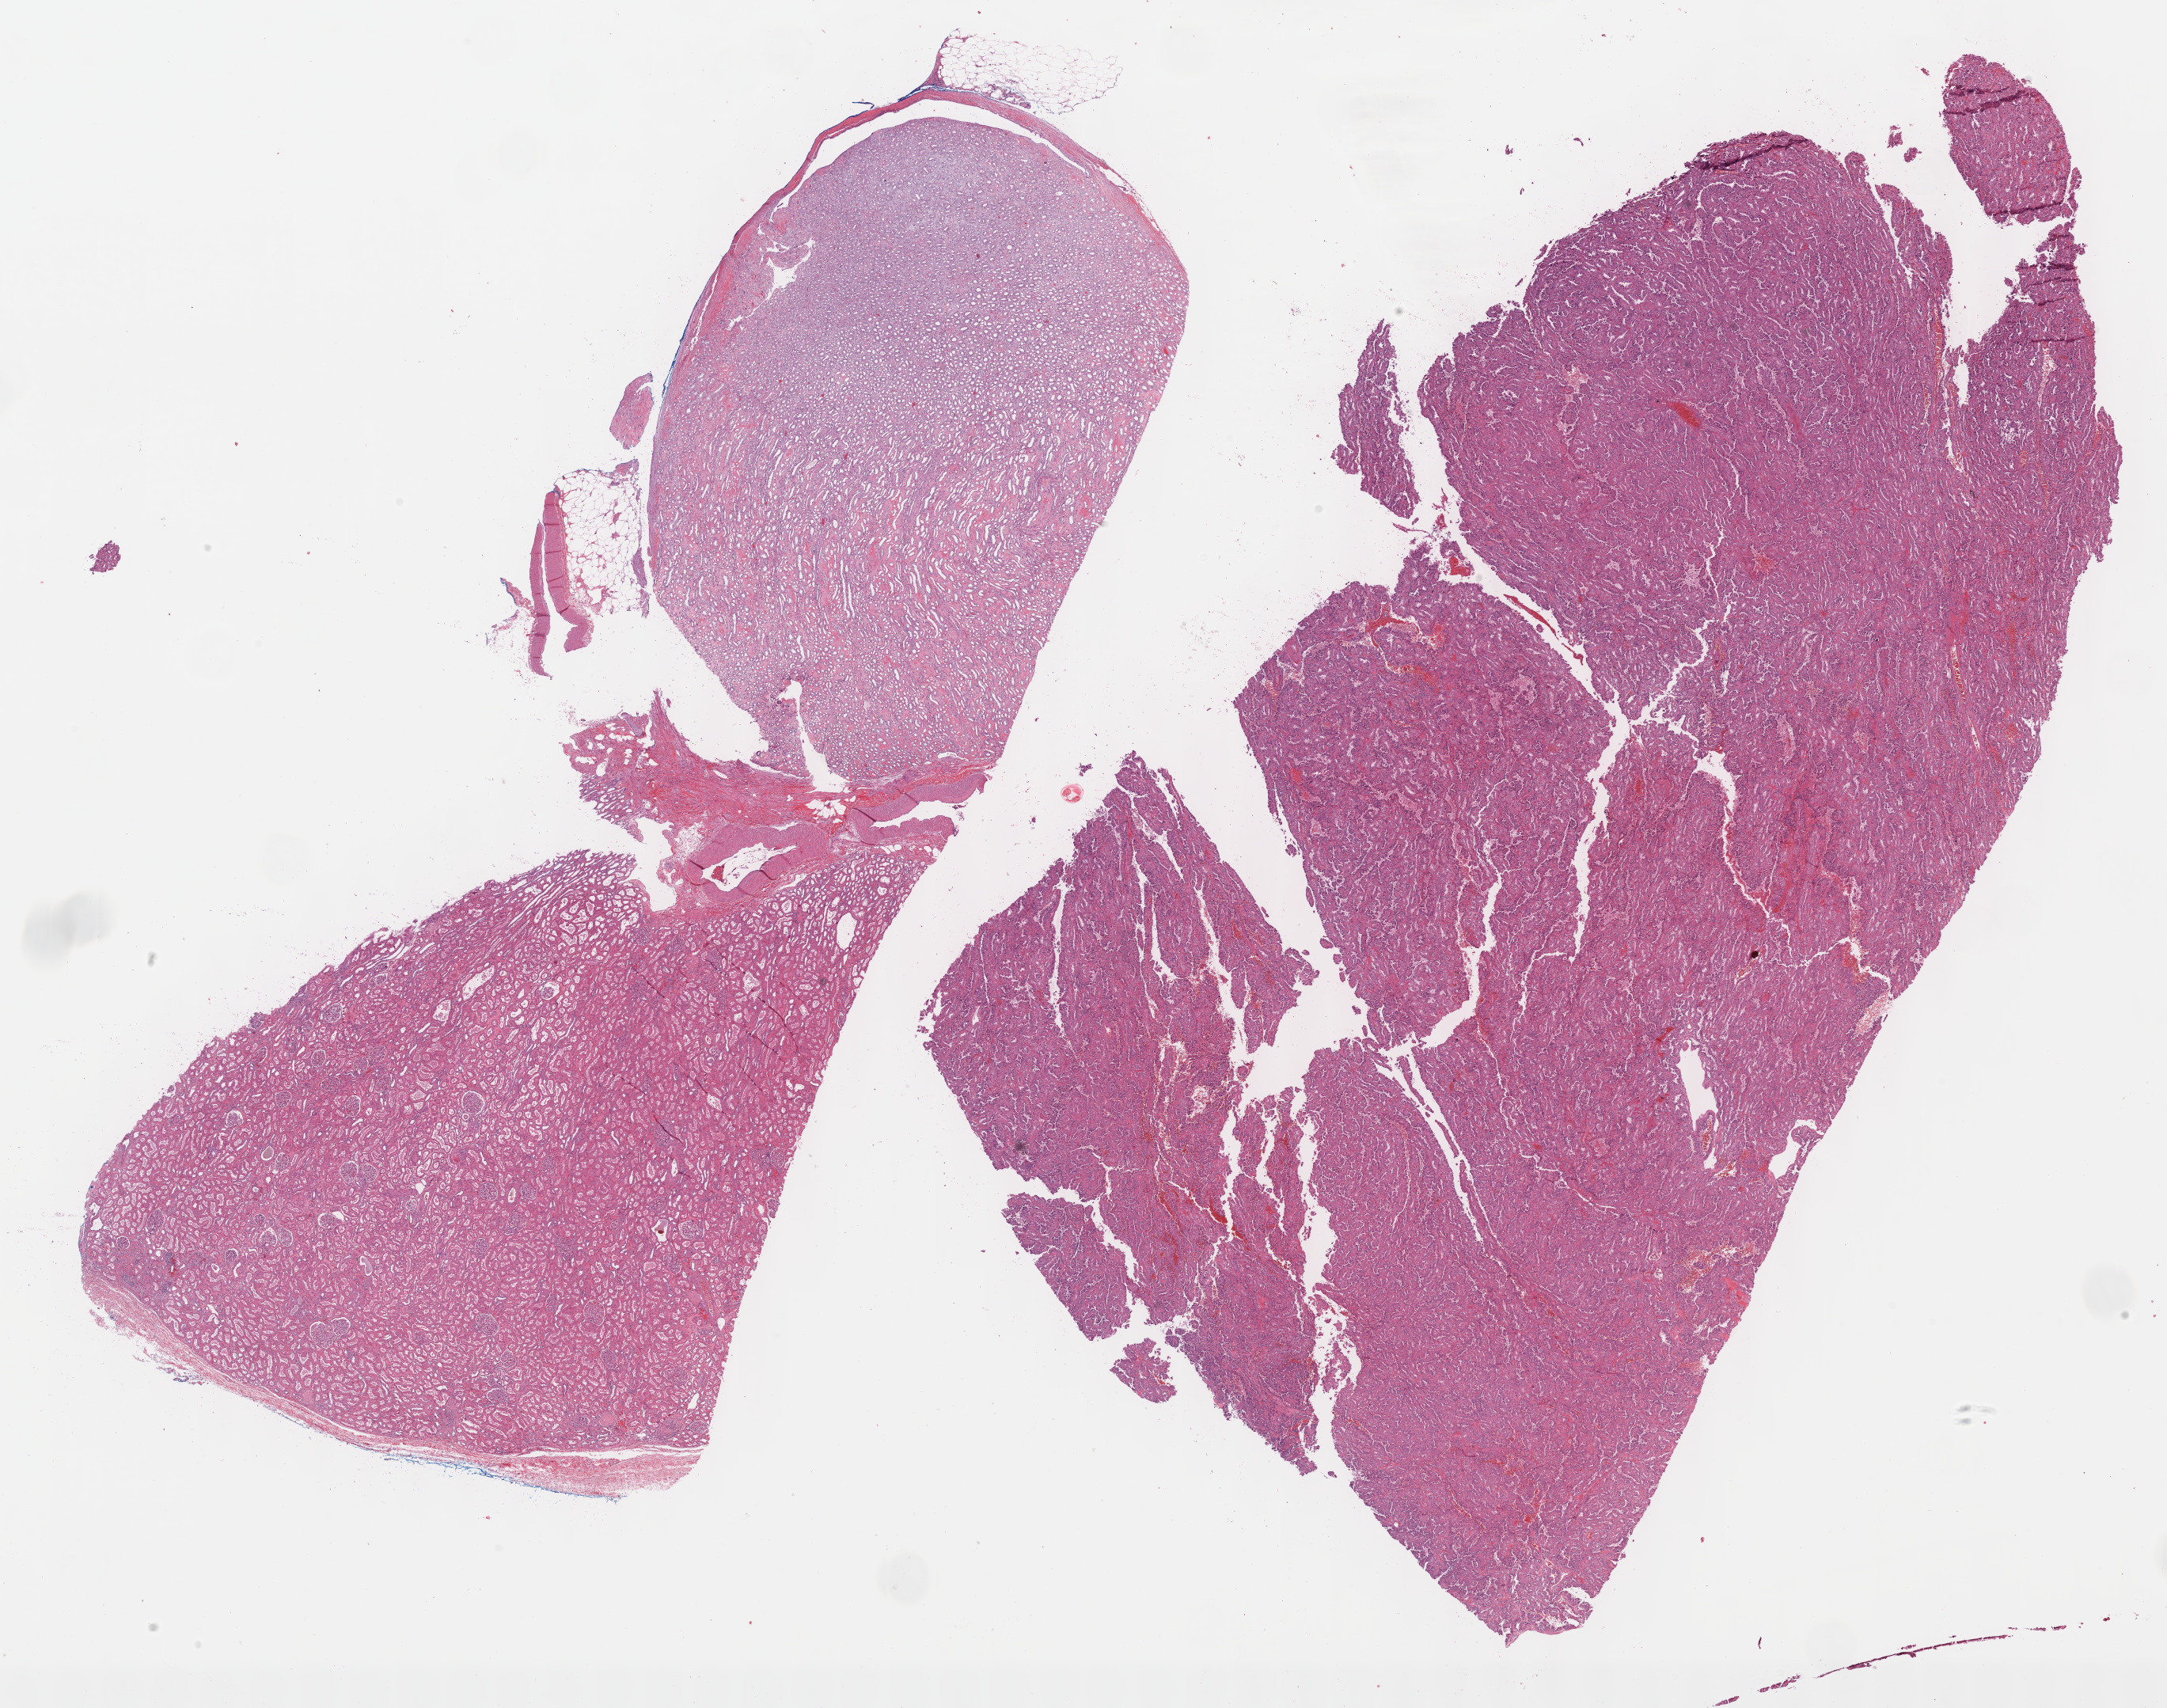
Hematoxylin and eosin (H&E) stained whole-slide image — whole scanned area (about 22.1 x 17.5 mm) shown as a low-resolution overview, formalin-fixed paraffin-embedded (FFPE) diagnostic section, kidney, primary tumour sample. Male patient; age at initial diagnosis 64 years.
TNM: T1b NX M0. Histologic diagnosis: Papillary adenocarcinoma, NOS. AJCC pathologic stage: I (7th edition).